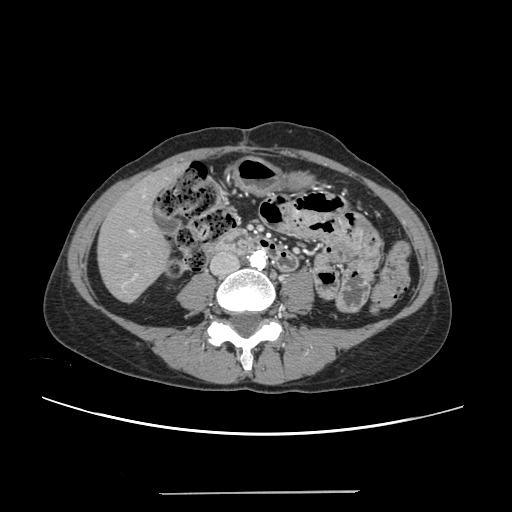
Contrast-enhanced abdominal CT, one axial slice; slice 57 of 240 in the series (ordered by position); 120 kVp; intravenous contrast given; soft-tissue window (W 400 / L 40 HU); 1.25 mm slice thickness; 512 × 512 image matrix, field of view 371 × 371 mm. Female patient, age 60 years. From the clinical record (not read from this slice): diagnosis: colorectal cancer liver metastases, imaged before liver resection; multiple liver metastases: no; largest metastasis: 1.5 cm; disease in both lobes: no.
Structures marked on this image (outlined manually by an expert reader):
- liver: bounding box (x1, y1, x2, y2) in pixels: (99, 168, 180, 301)
- planned liver remnant (the part of the liver to remain after resection): (99, 171, 171, 301)
- portal vein (with intrahepatic branches): (123, 188, 147, 287)